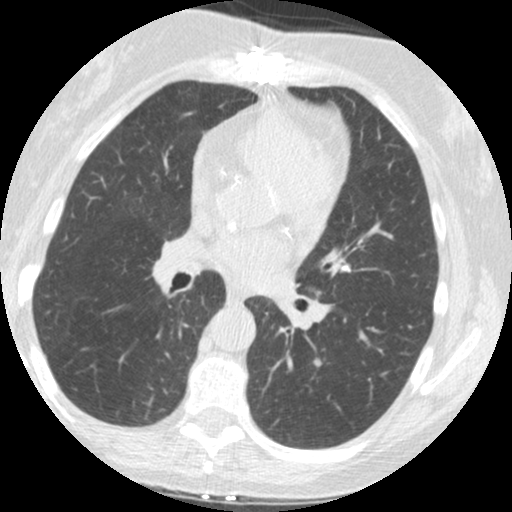
Chest CT (low-dose screening protocol), one axial image. First (baseline) screen. Lung window (W 1500 / L -600 HU). 2.5 mm slice thickness. Slice 71 of 147 in the series. 512 × 512 image matrix. Female, age 61 years at enrolment.
- Expert reader's lesion annotation, box from (x=300, y=335) to (x=348, y=392) px.
- The exam's reader record, not a measurement of the box and not confirmed to be the same lesion: non-calcified nodule or mass ≥4 mm, left lower lobe, 12 × 11 mm, spiculated (stellate) margins, soft tissue attenuation.
- Official screen result: positive, change unspecified: nodule(s) >= 4 mm or enlarging nodule(s), mass(es), or other non-specific abnormalities suspicious for lung cancer.
- Later outcome: lung cancer diagnosed 440 days after this screen (after the second annual screen) — squamous cell carcinoma, NOS, left lower lobe, moderately differentiated (G2), stage IA (AJCC 6th edition), 12 mm at pathology.